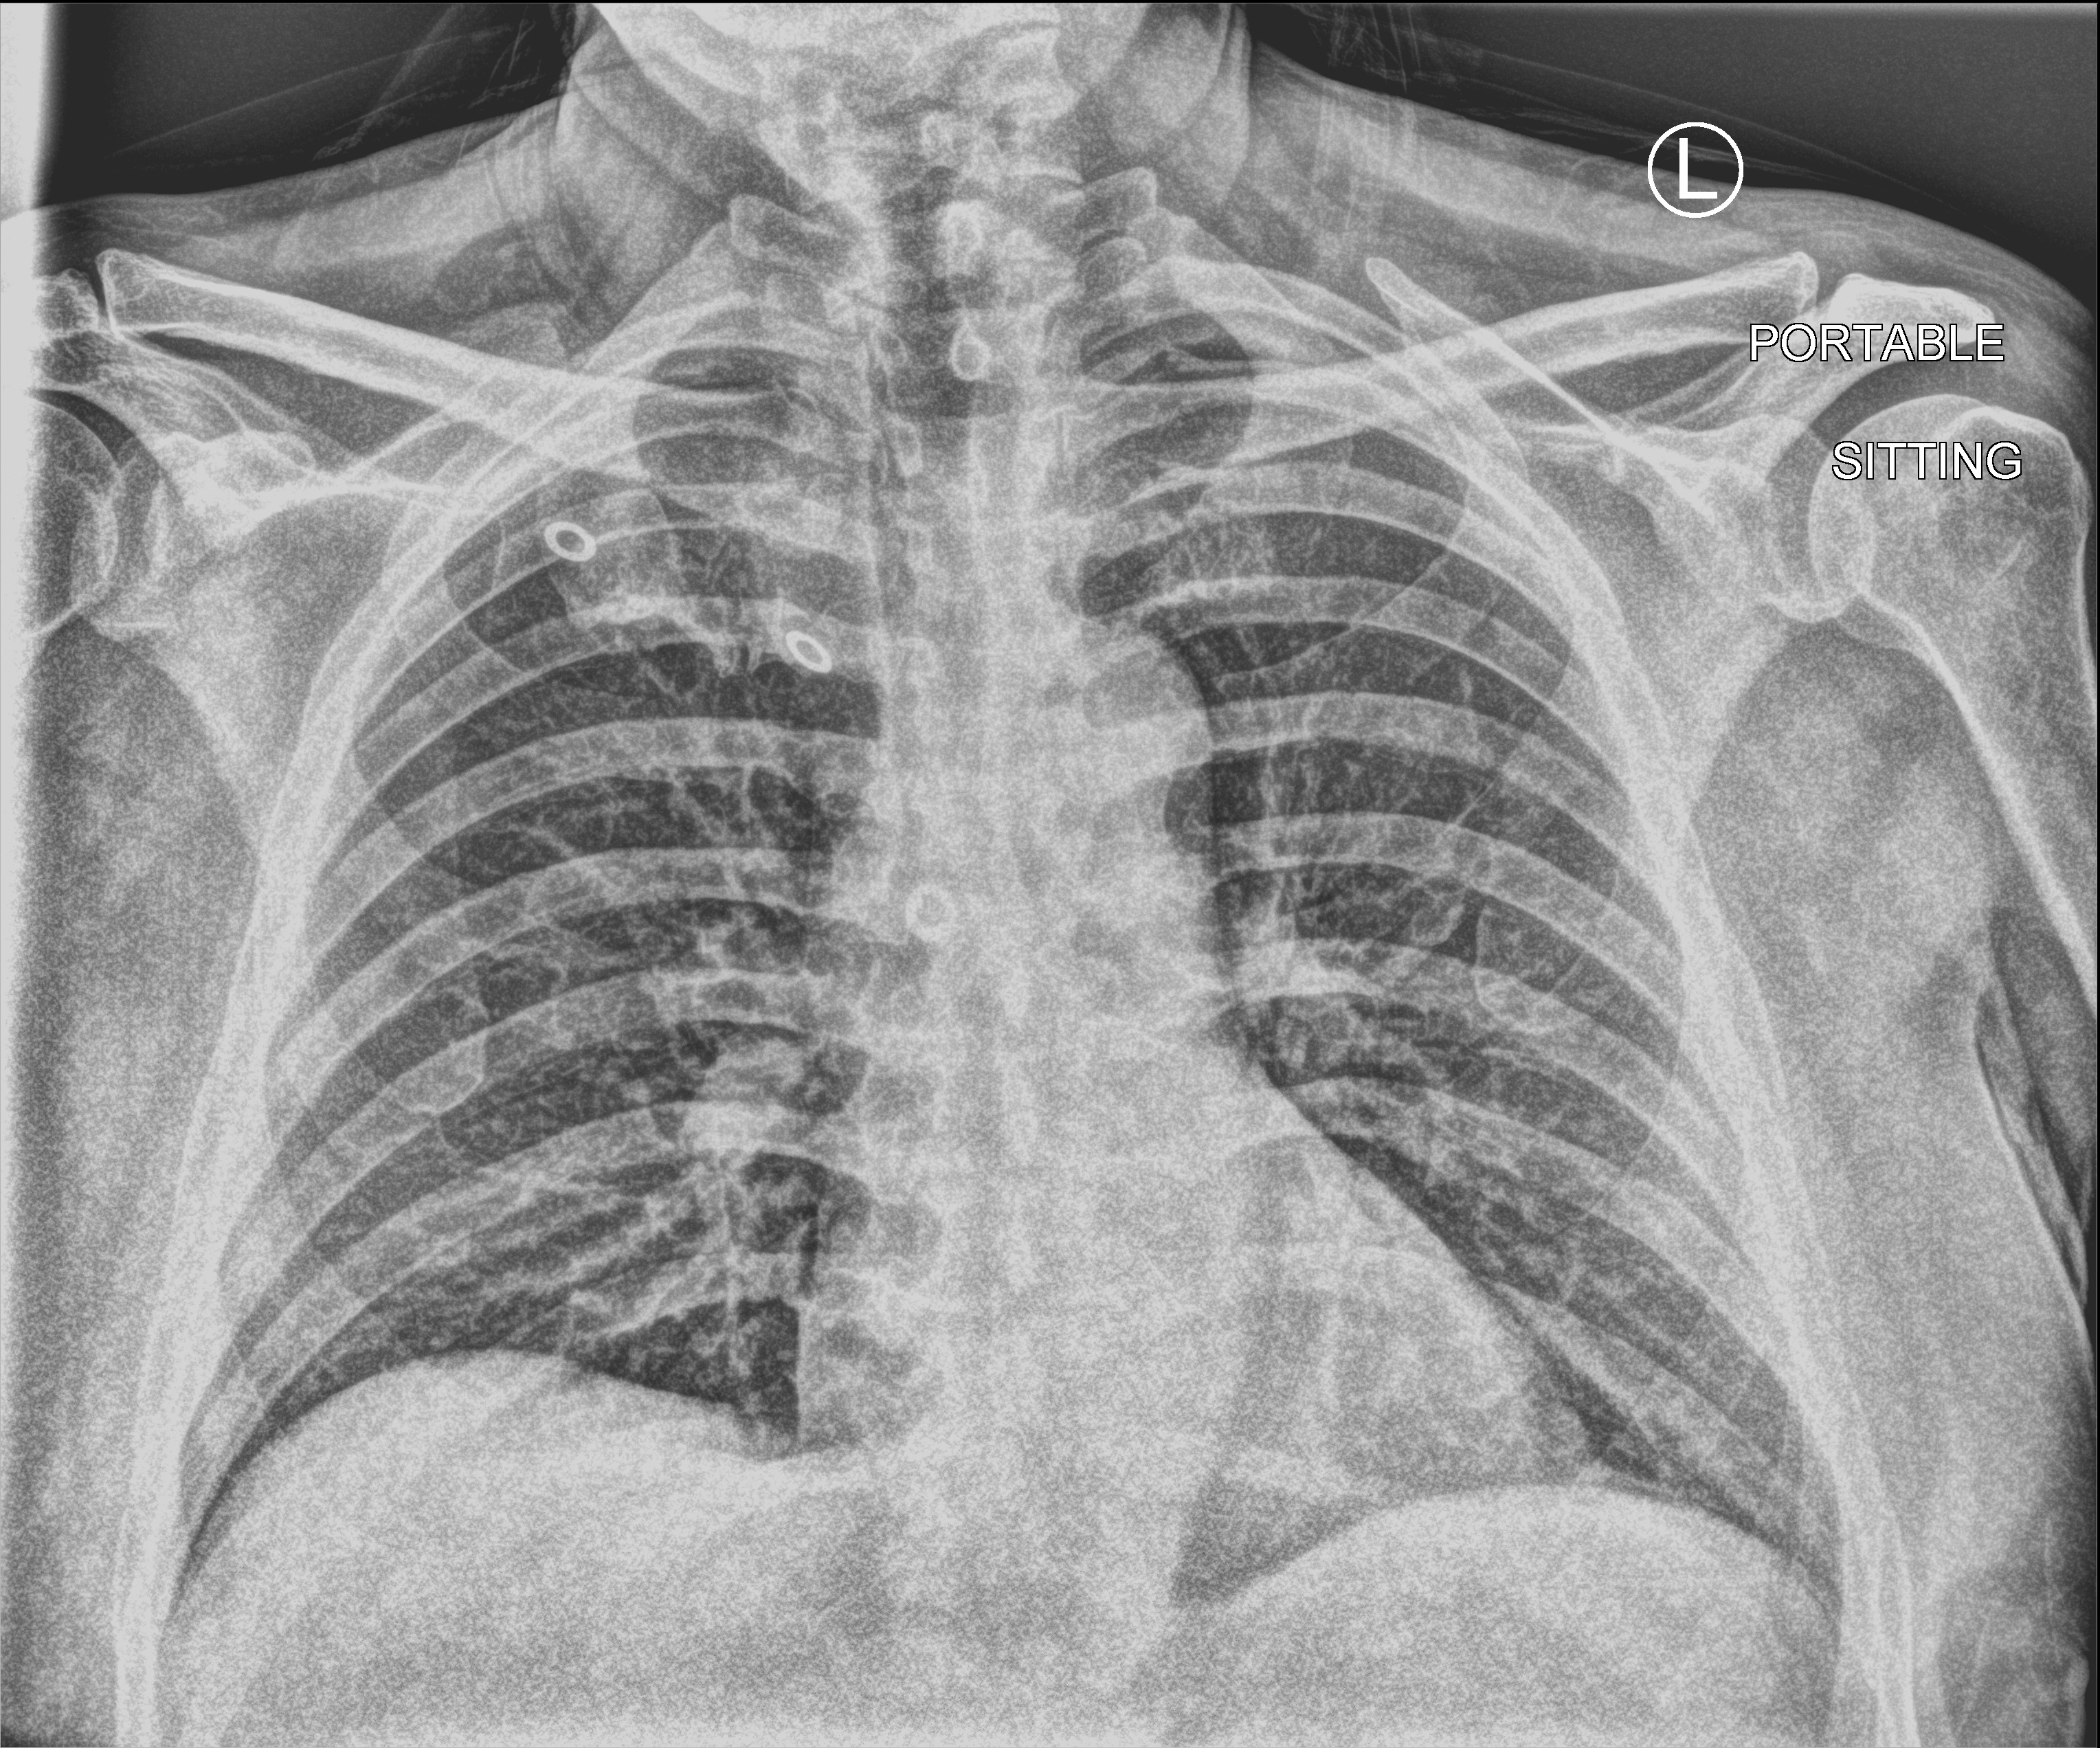
Bedside chest radiograph (computed radiography); anteroposterior (AP) projection. Male patient hospitalised with COVID-19, age 60–74 years.
From the hospital-stay record, not from the radiograph (when in the stay this image was taken is not recorded):
- hypertension (admission record): yes
- admitted to intensive care during this hospital stay: no